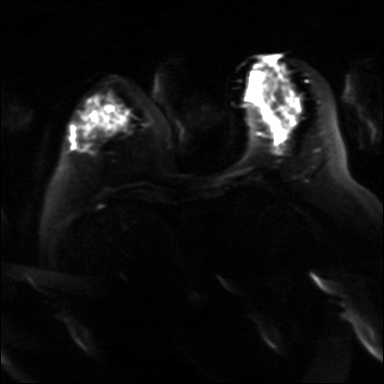
Breast MRI, one axial slice. Slice 10 of 36 in the series (ordered by position). Diffusion-weighted series; image 2 of 4 stored at this slice position (different b-values; order by instance number). 3 T. 4 mm slice thickness. 384 × 384 image matrix, field of view 320 × 320 mm. Female patient.
Outlined on this slice (outlined manually by an expert reader):
- tumour on diffusion-weighted imaging: bounding box (x1, y1, x2, y2) in pixels: (292, 121, 299, 125)